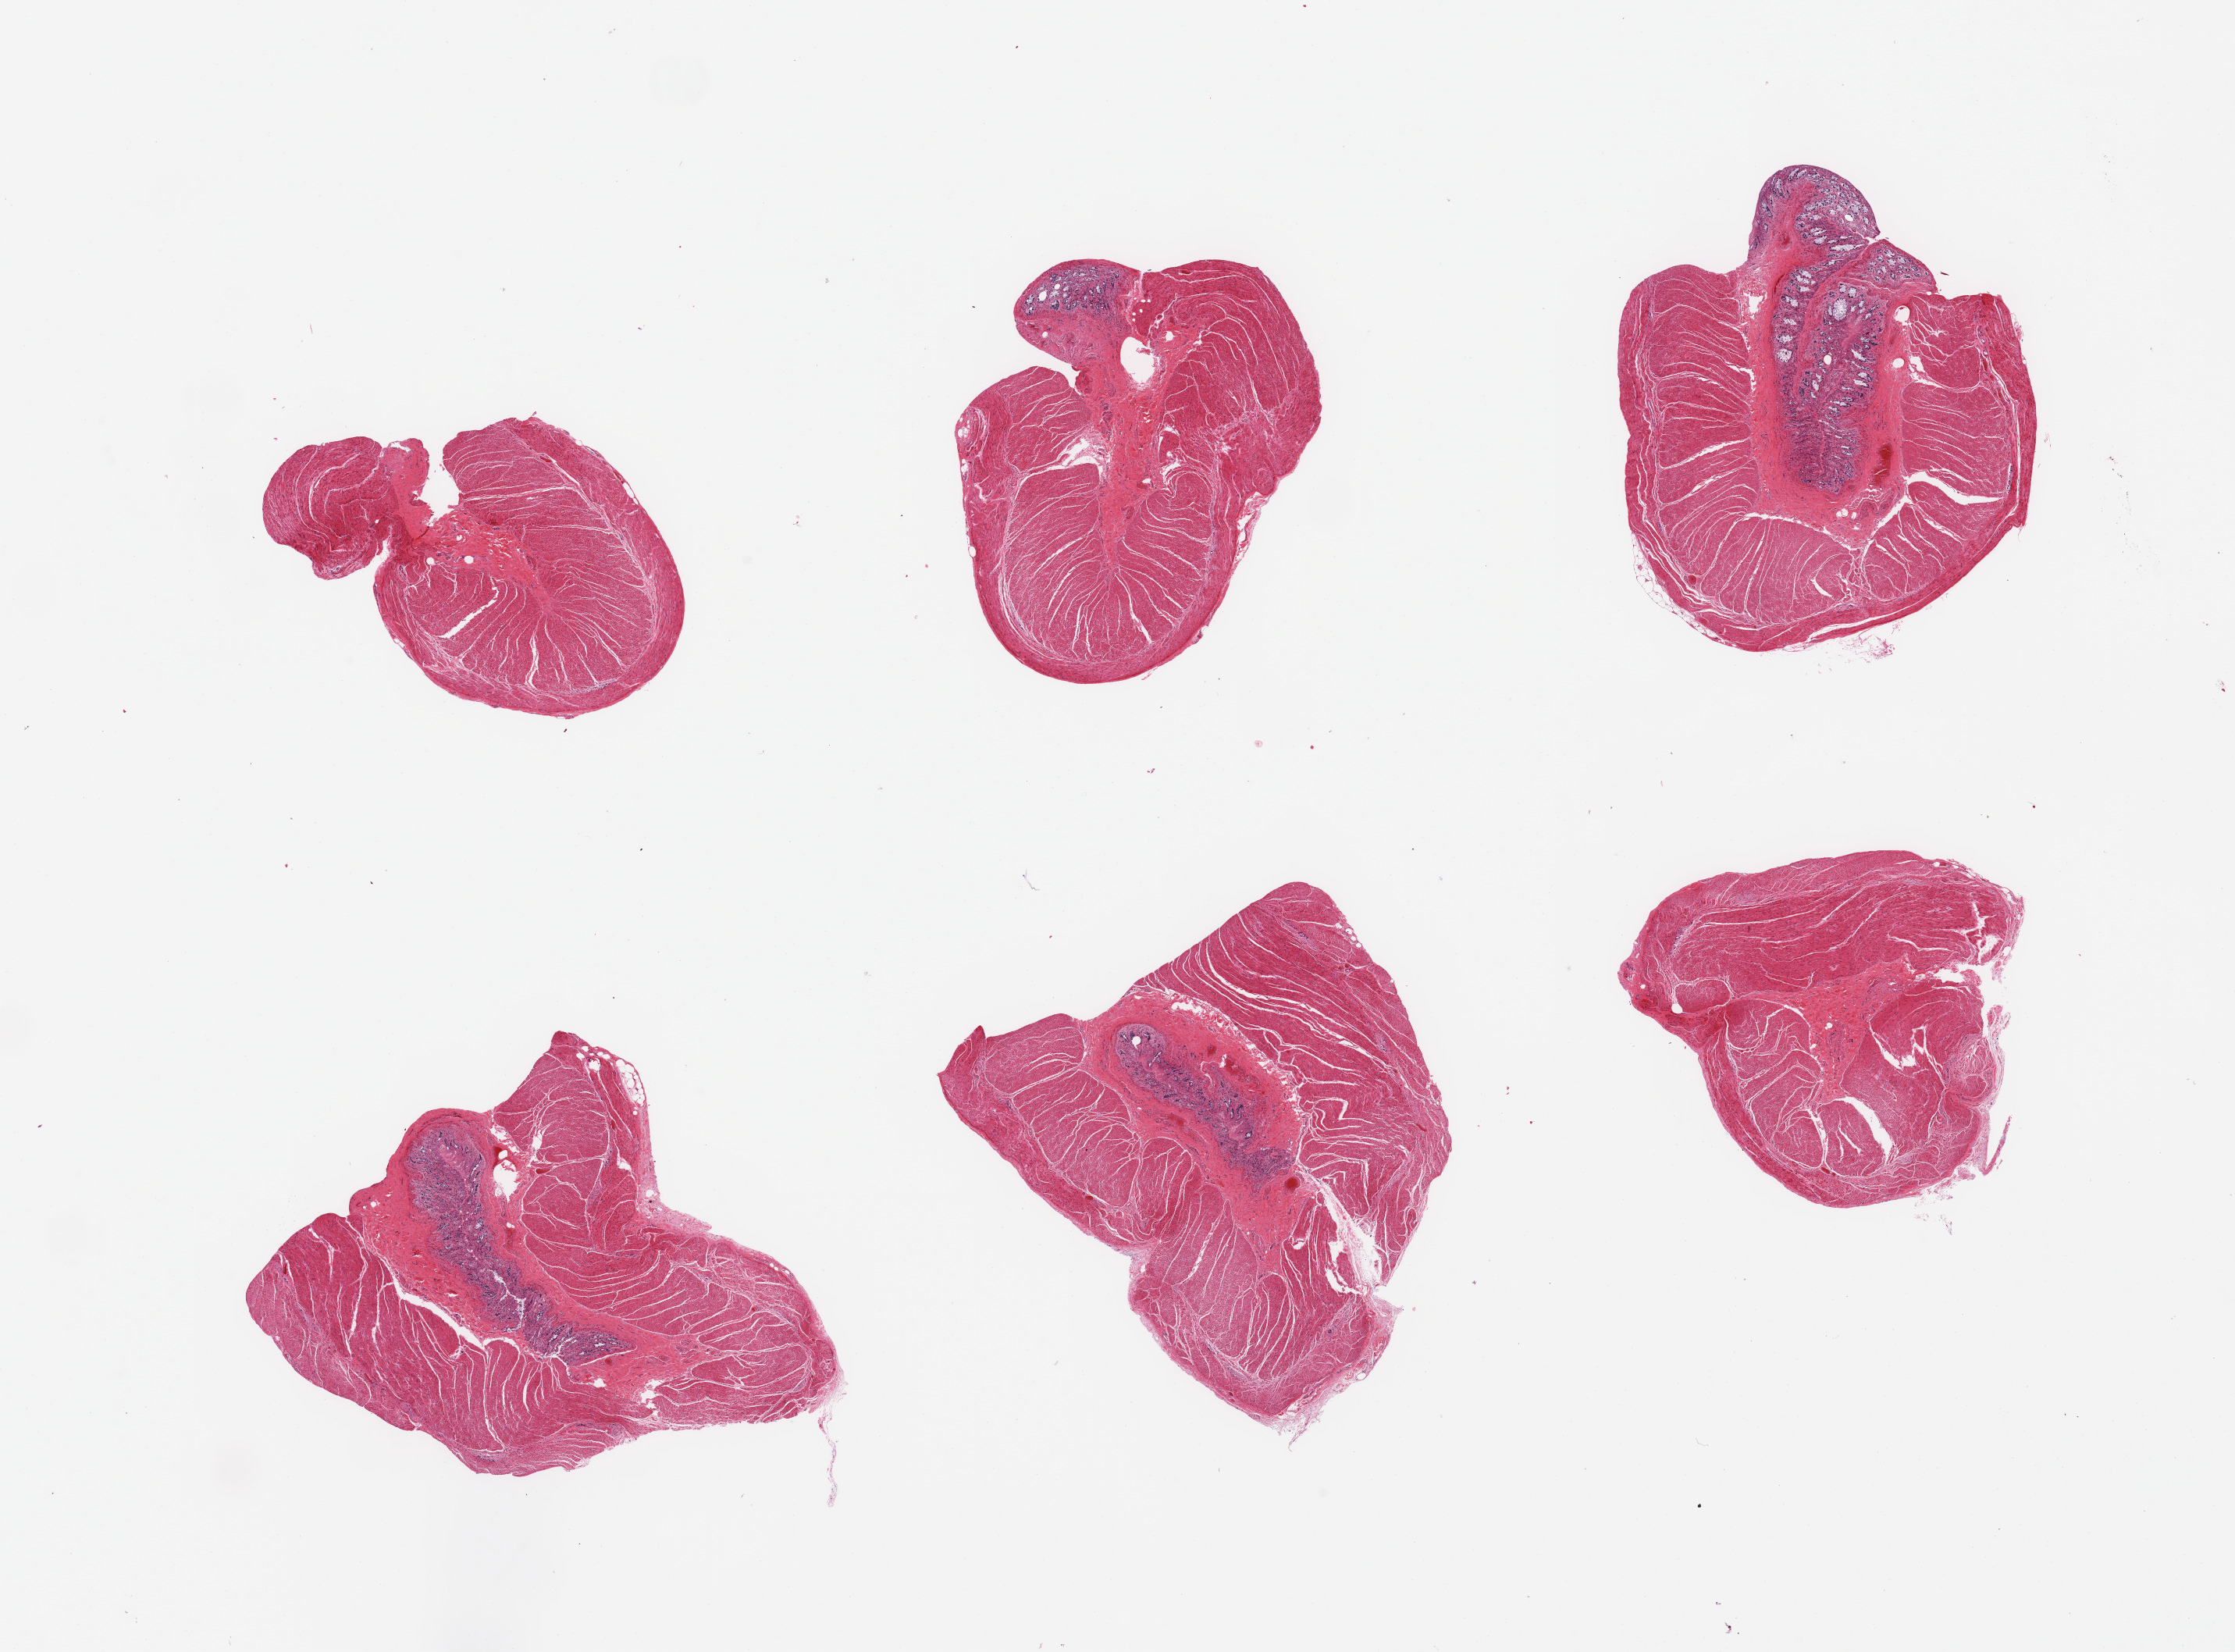
Digitized hematoxylin and eosin (H&E)-stained section, brightfield, a low-resolution overview of the entire scanned area, about 22.6 x 16.7 mm (slide scanned at 20x). PAXgene-fixed, paraffin-embedded tissue. Sampled site (target tissue): sigmoid colon. Donor tissue sample. Donor: female.
* review note (as recorded): 6 pieces; predominantly muscularis, 4 include strips of largely autolyzed mucosa